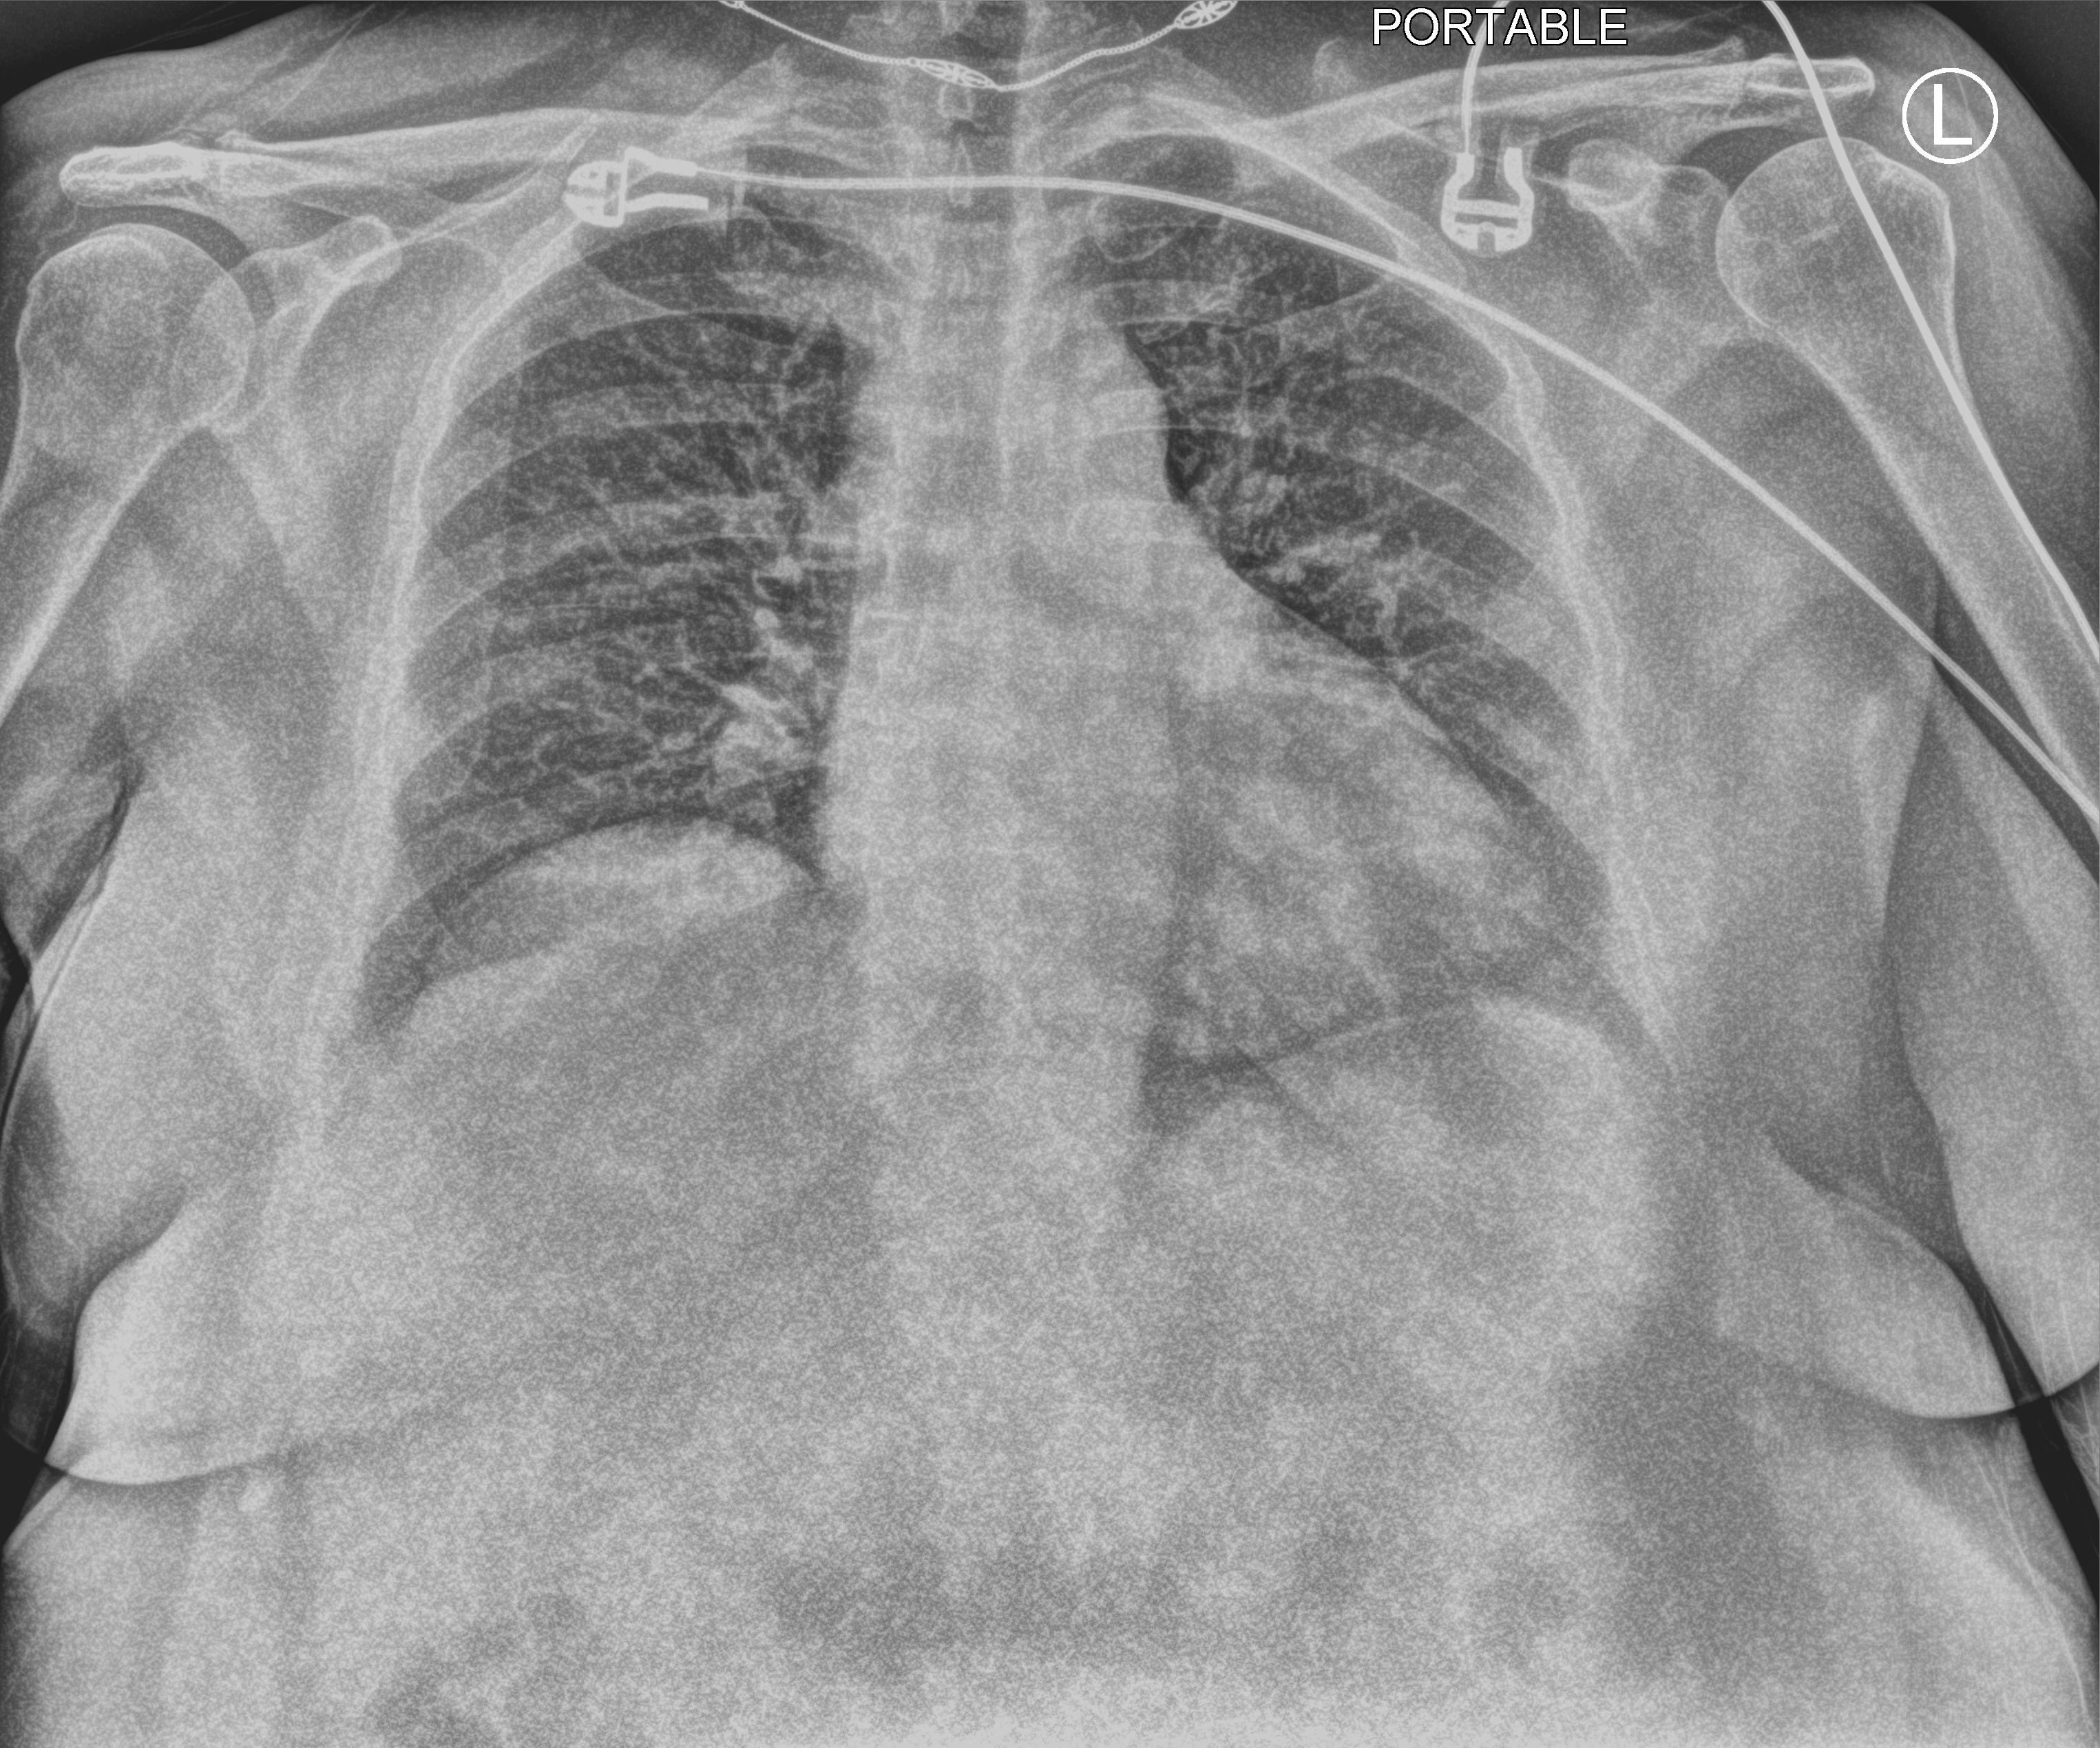
Chest X-ray (portable); anteroposterior (AP) projection. Patient hospitalised with COVID-19, aged 60–74 years.
Admission-level facts for this patient (not findings on this image; timing relative to this image not recorded): chronic kidney disease (admission record): no.